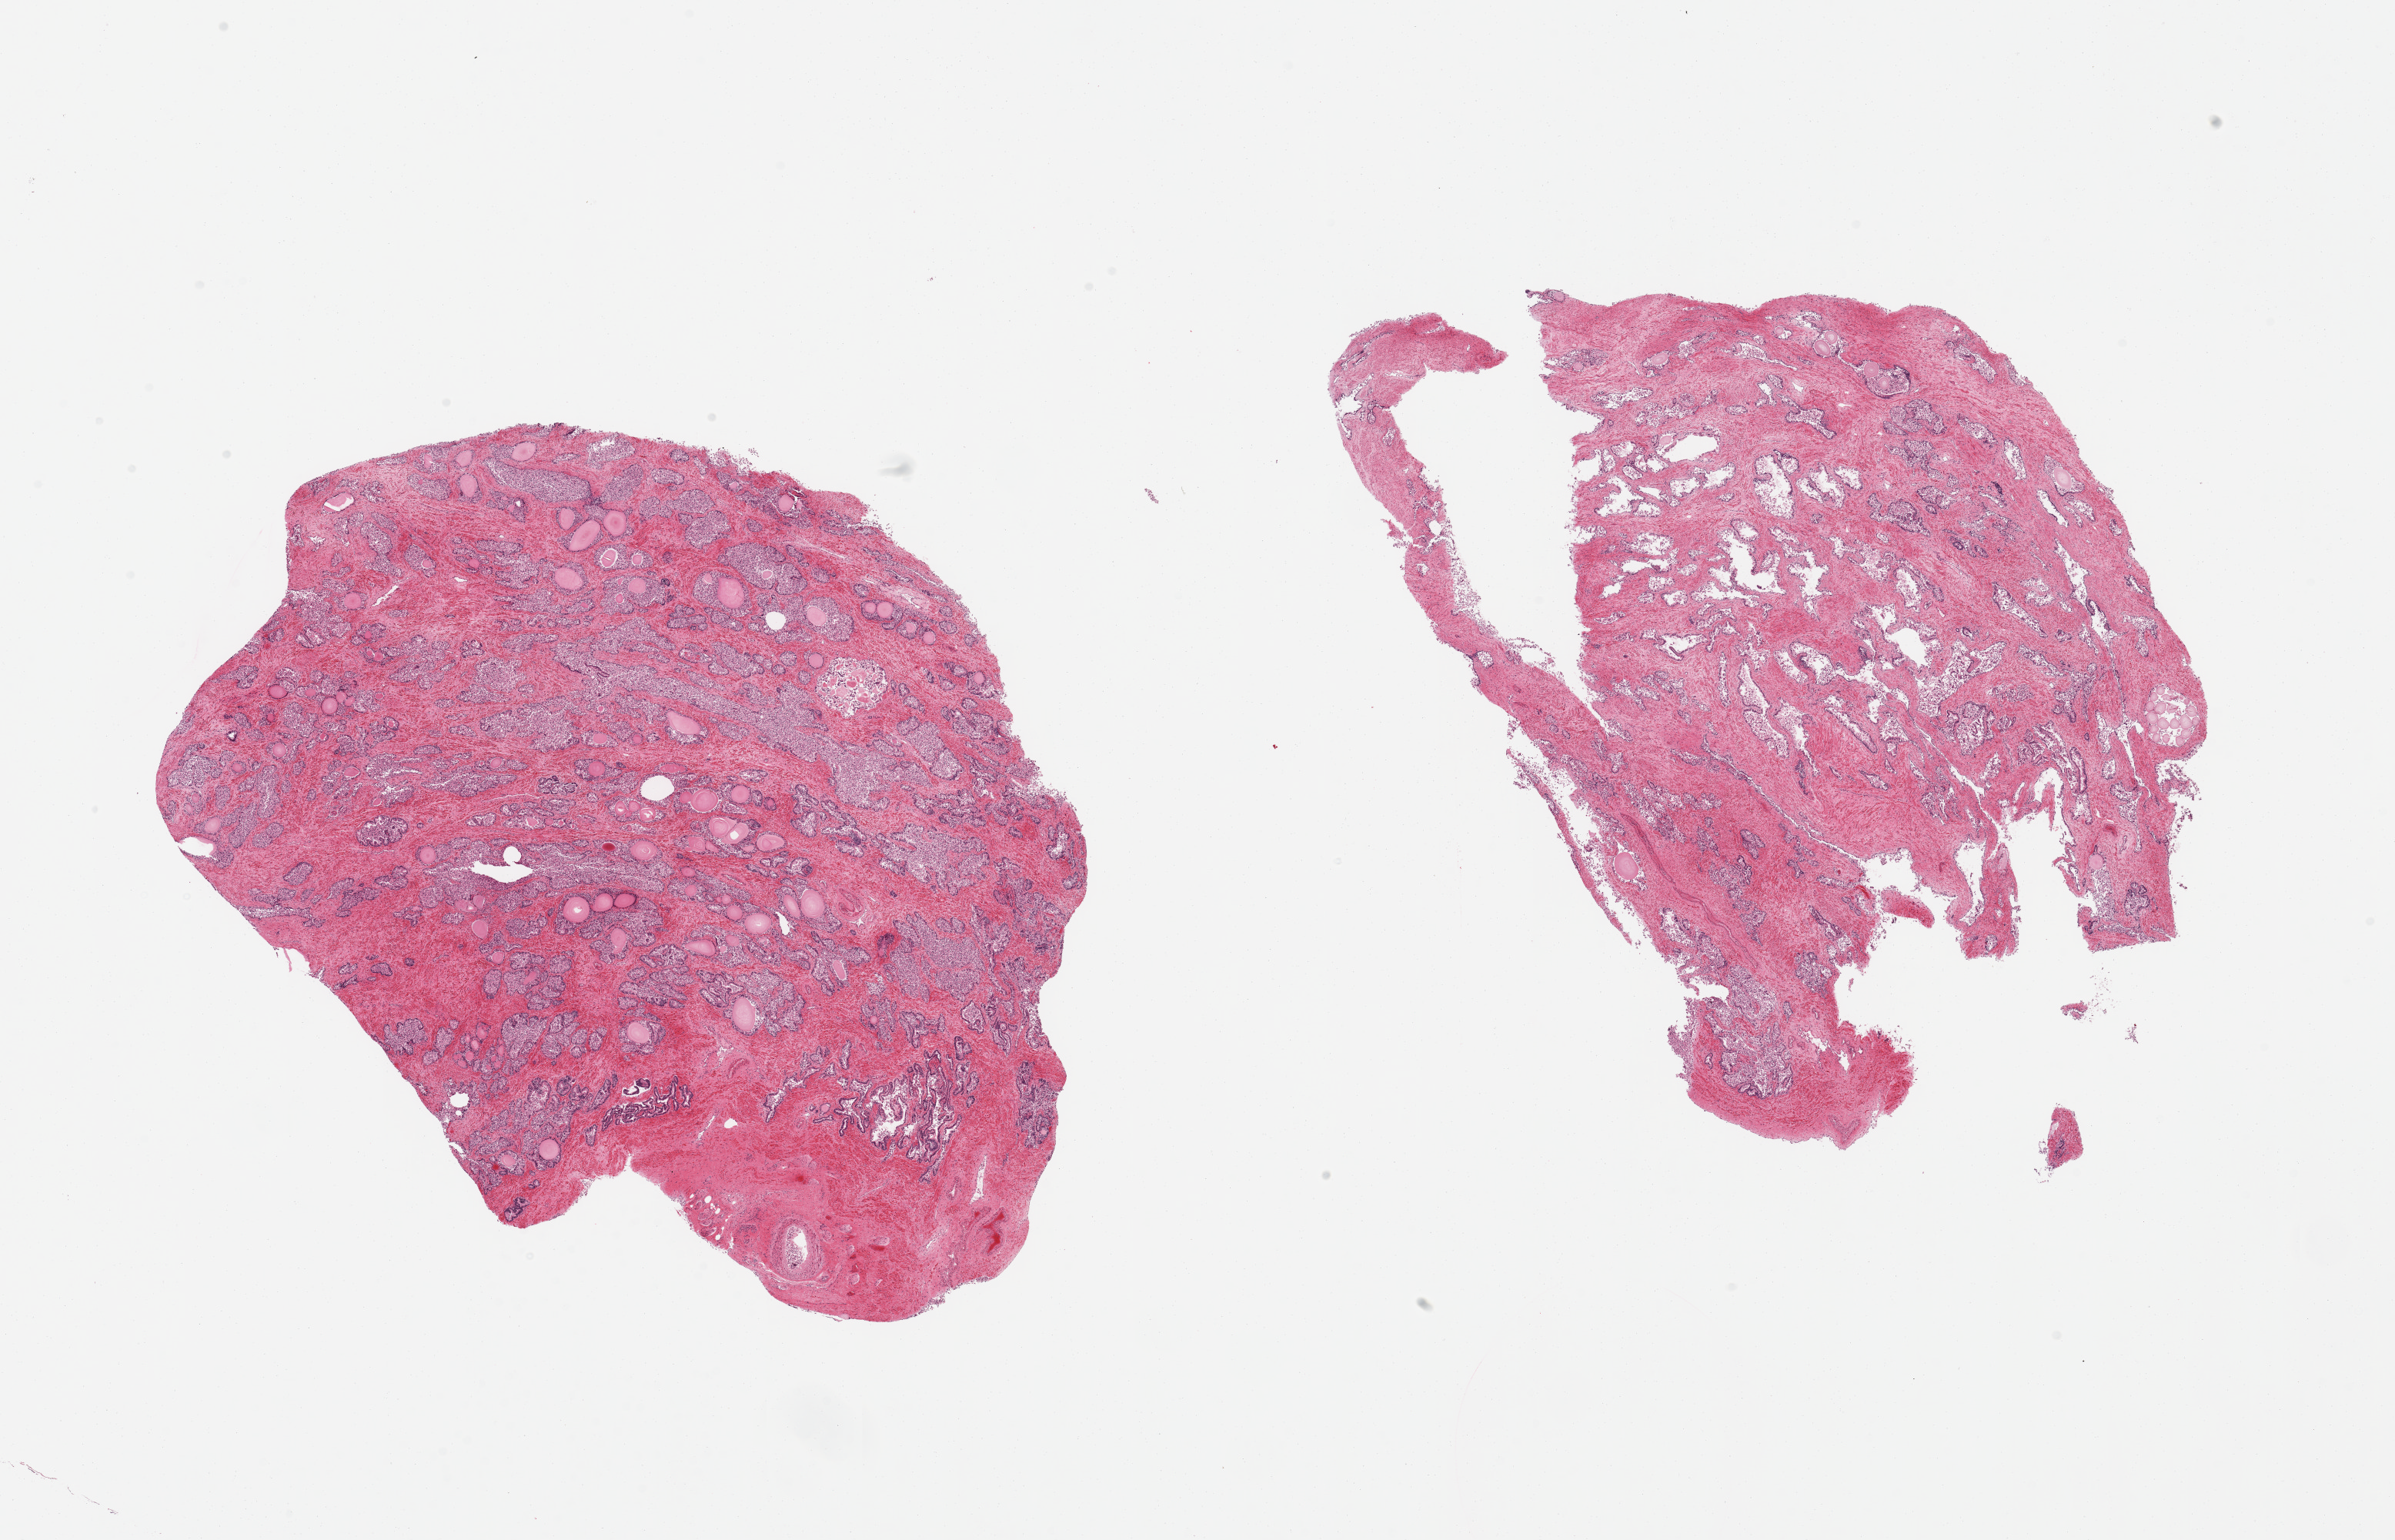
H&E whole-slide image — shown as a low-resolution overview of the whole scanned area (about 24.6 x 15.8 mm, slide scanned at 20x). PAXgene-fixed, paraffin-embedded tissue. Section of prostate (target tissue). Tissue donor sample. Donor: male.
Review note (as recorded): 2 pieces; glands largely autolyzed; stroma intact.